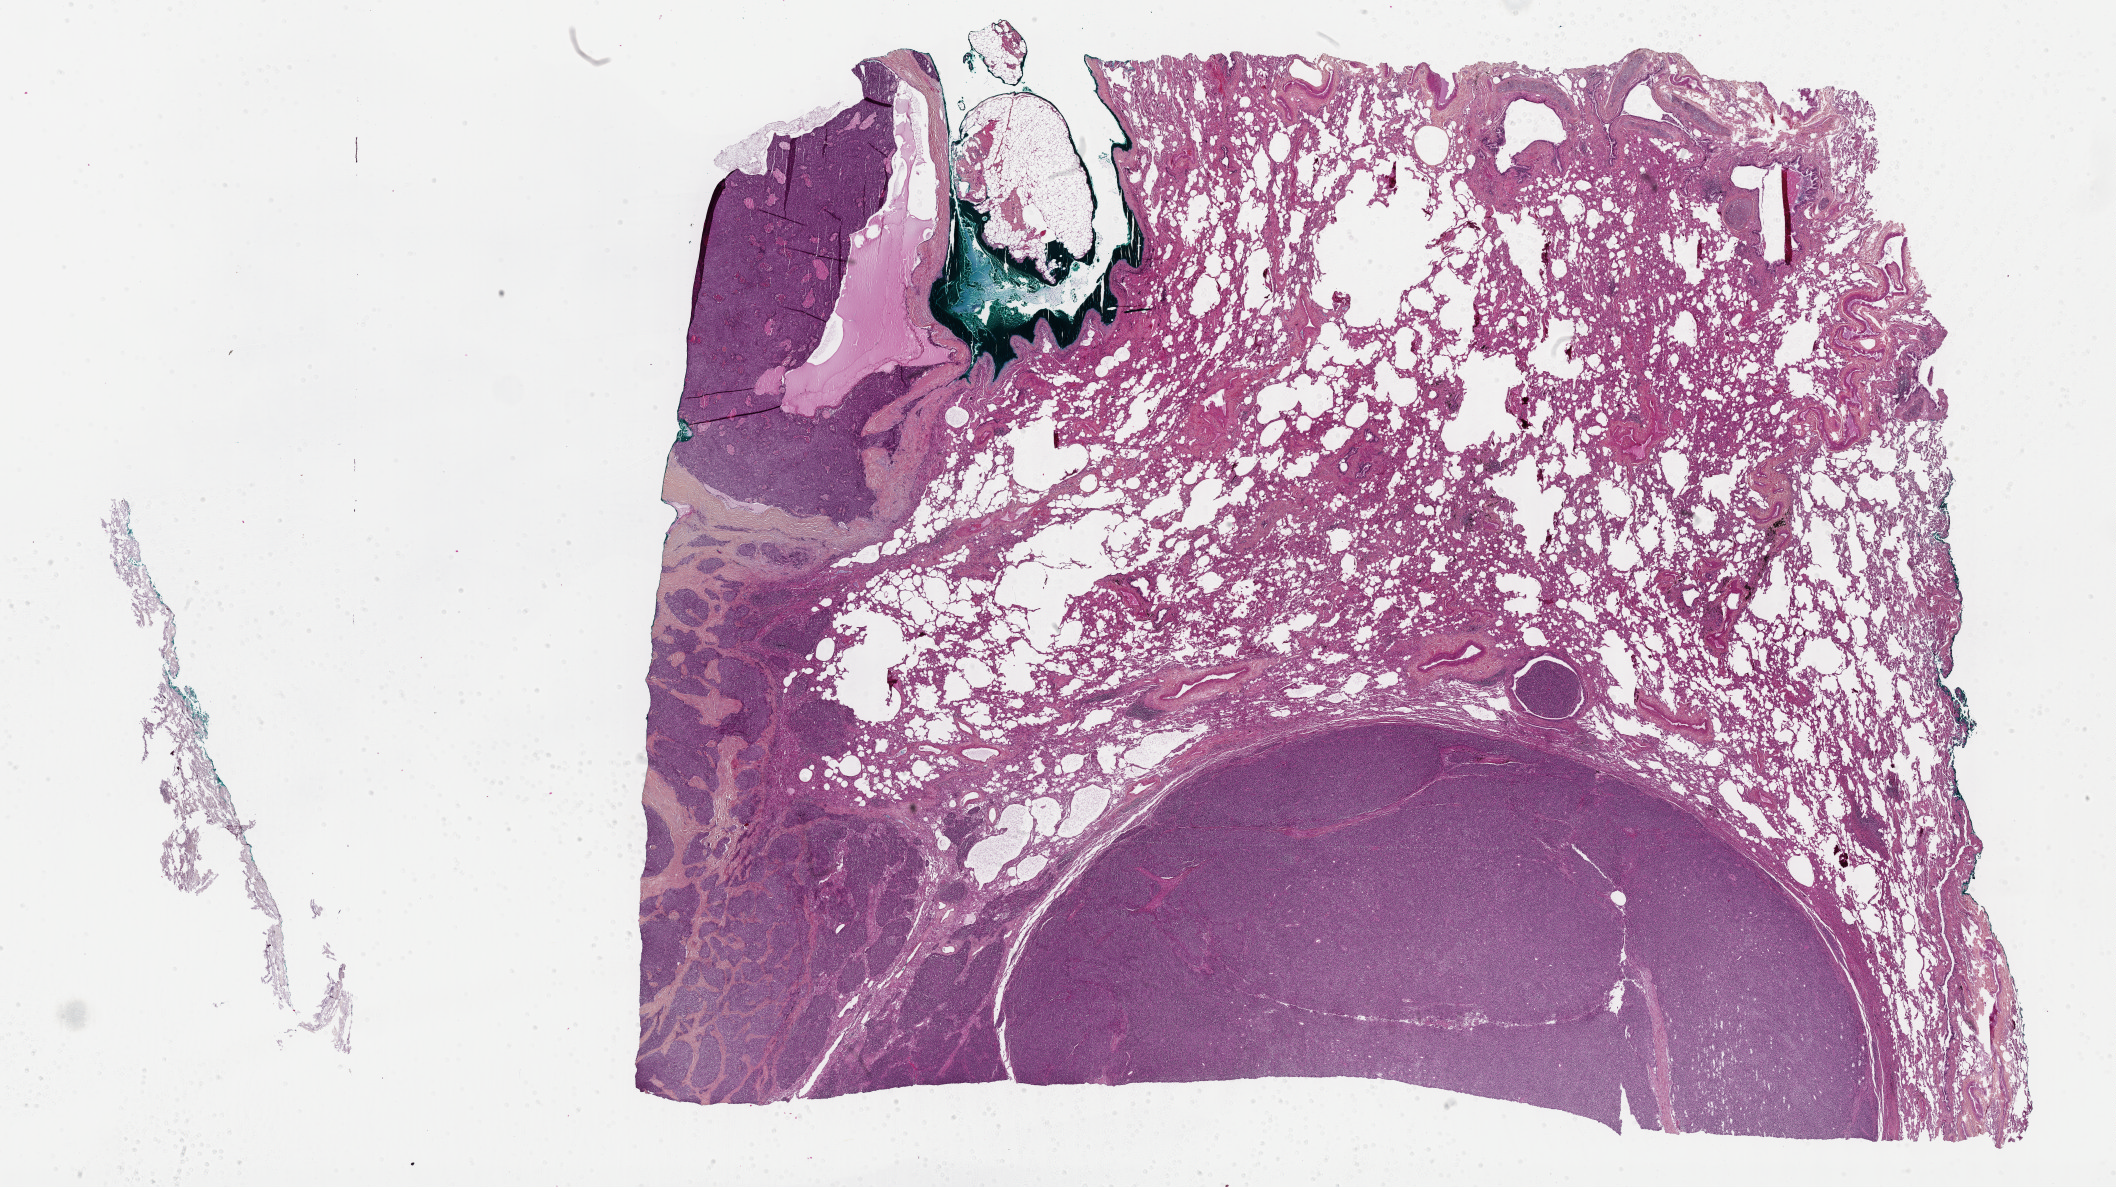
Digitized H&E tissue section (whole slide), a low-resolution overview of the entire scanned area, about 34.2 x 19.2 mm (slide scanned at 40x). FFPE section. Thymus, primary tumour sample. Patient: female, age at initial diagnosis 51 years.
* histologic diagnosis: Thymoma, type B3, malignant